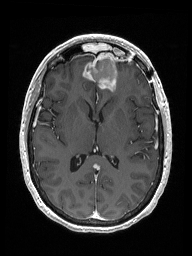
Brain MRI from a brain-tumour surgery series, one axial slice. Slice 82 of 192 in the series (ordered by position). T1-weighted post-contrast. 192 × 256 image matrix, field of view 187 × 250 mm. Case-level facts recorded for this patient, not image findings: histopathology: Metastastic Carcinoma from Breast primary.
Structures marked on this image (outlined manually by an expert reader):
- previous resection cavity: bounding box <85,52,117,81> (left, top, right, bottom; pixels)